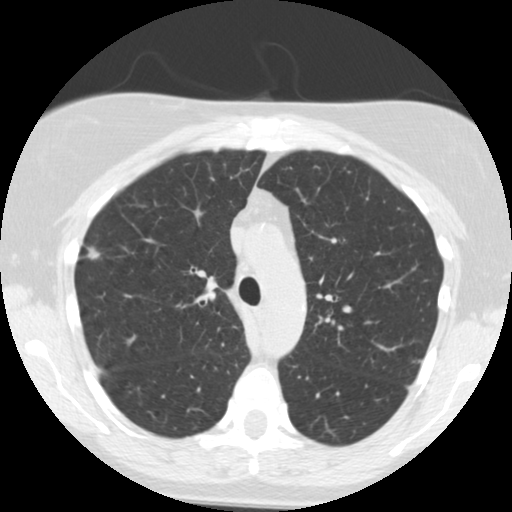
Chest CT (low-dose screening protocol), one axial image. Second annual screen. Lung window (W 1500 / L -600 HU). Slice 167 of 244 in the series. 512 × 512 image matrix, field of view 312 × 312 mm. Female participant, aged 55 years at enrolment.
Expert reader's lesion annotation, bounding box [x1, y1, x2, y2] px = [69, 237, 114, 278]. Screening reader's record for this exam: no non-calcified nodule ≥4 mm recorded. Official screen result: negative screen, minor abnormalities not suspicious for lung cancer. Participant outcome: lung cancer diagnosed 621 days after this screen — bronchiolo-alveolar adenocarcinoma, NOS, right upper lobe, moderately differentiated (G2), stage IIA (AJCC 6th edition), 13 mm at pathology.